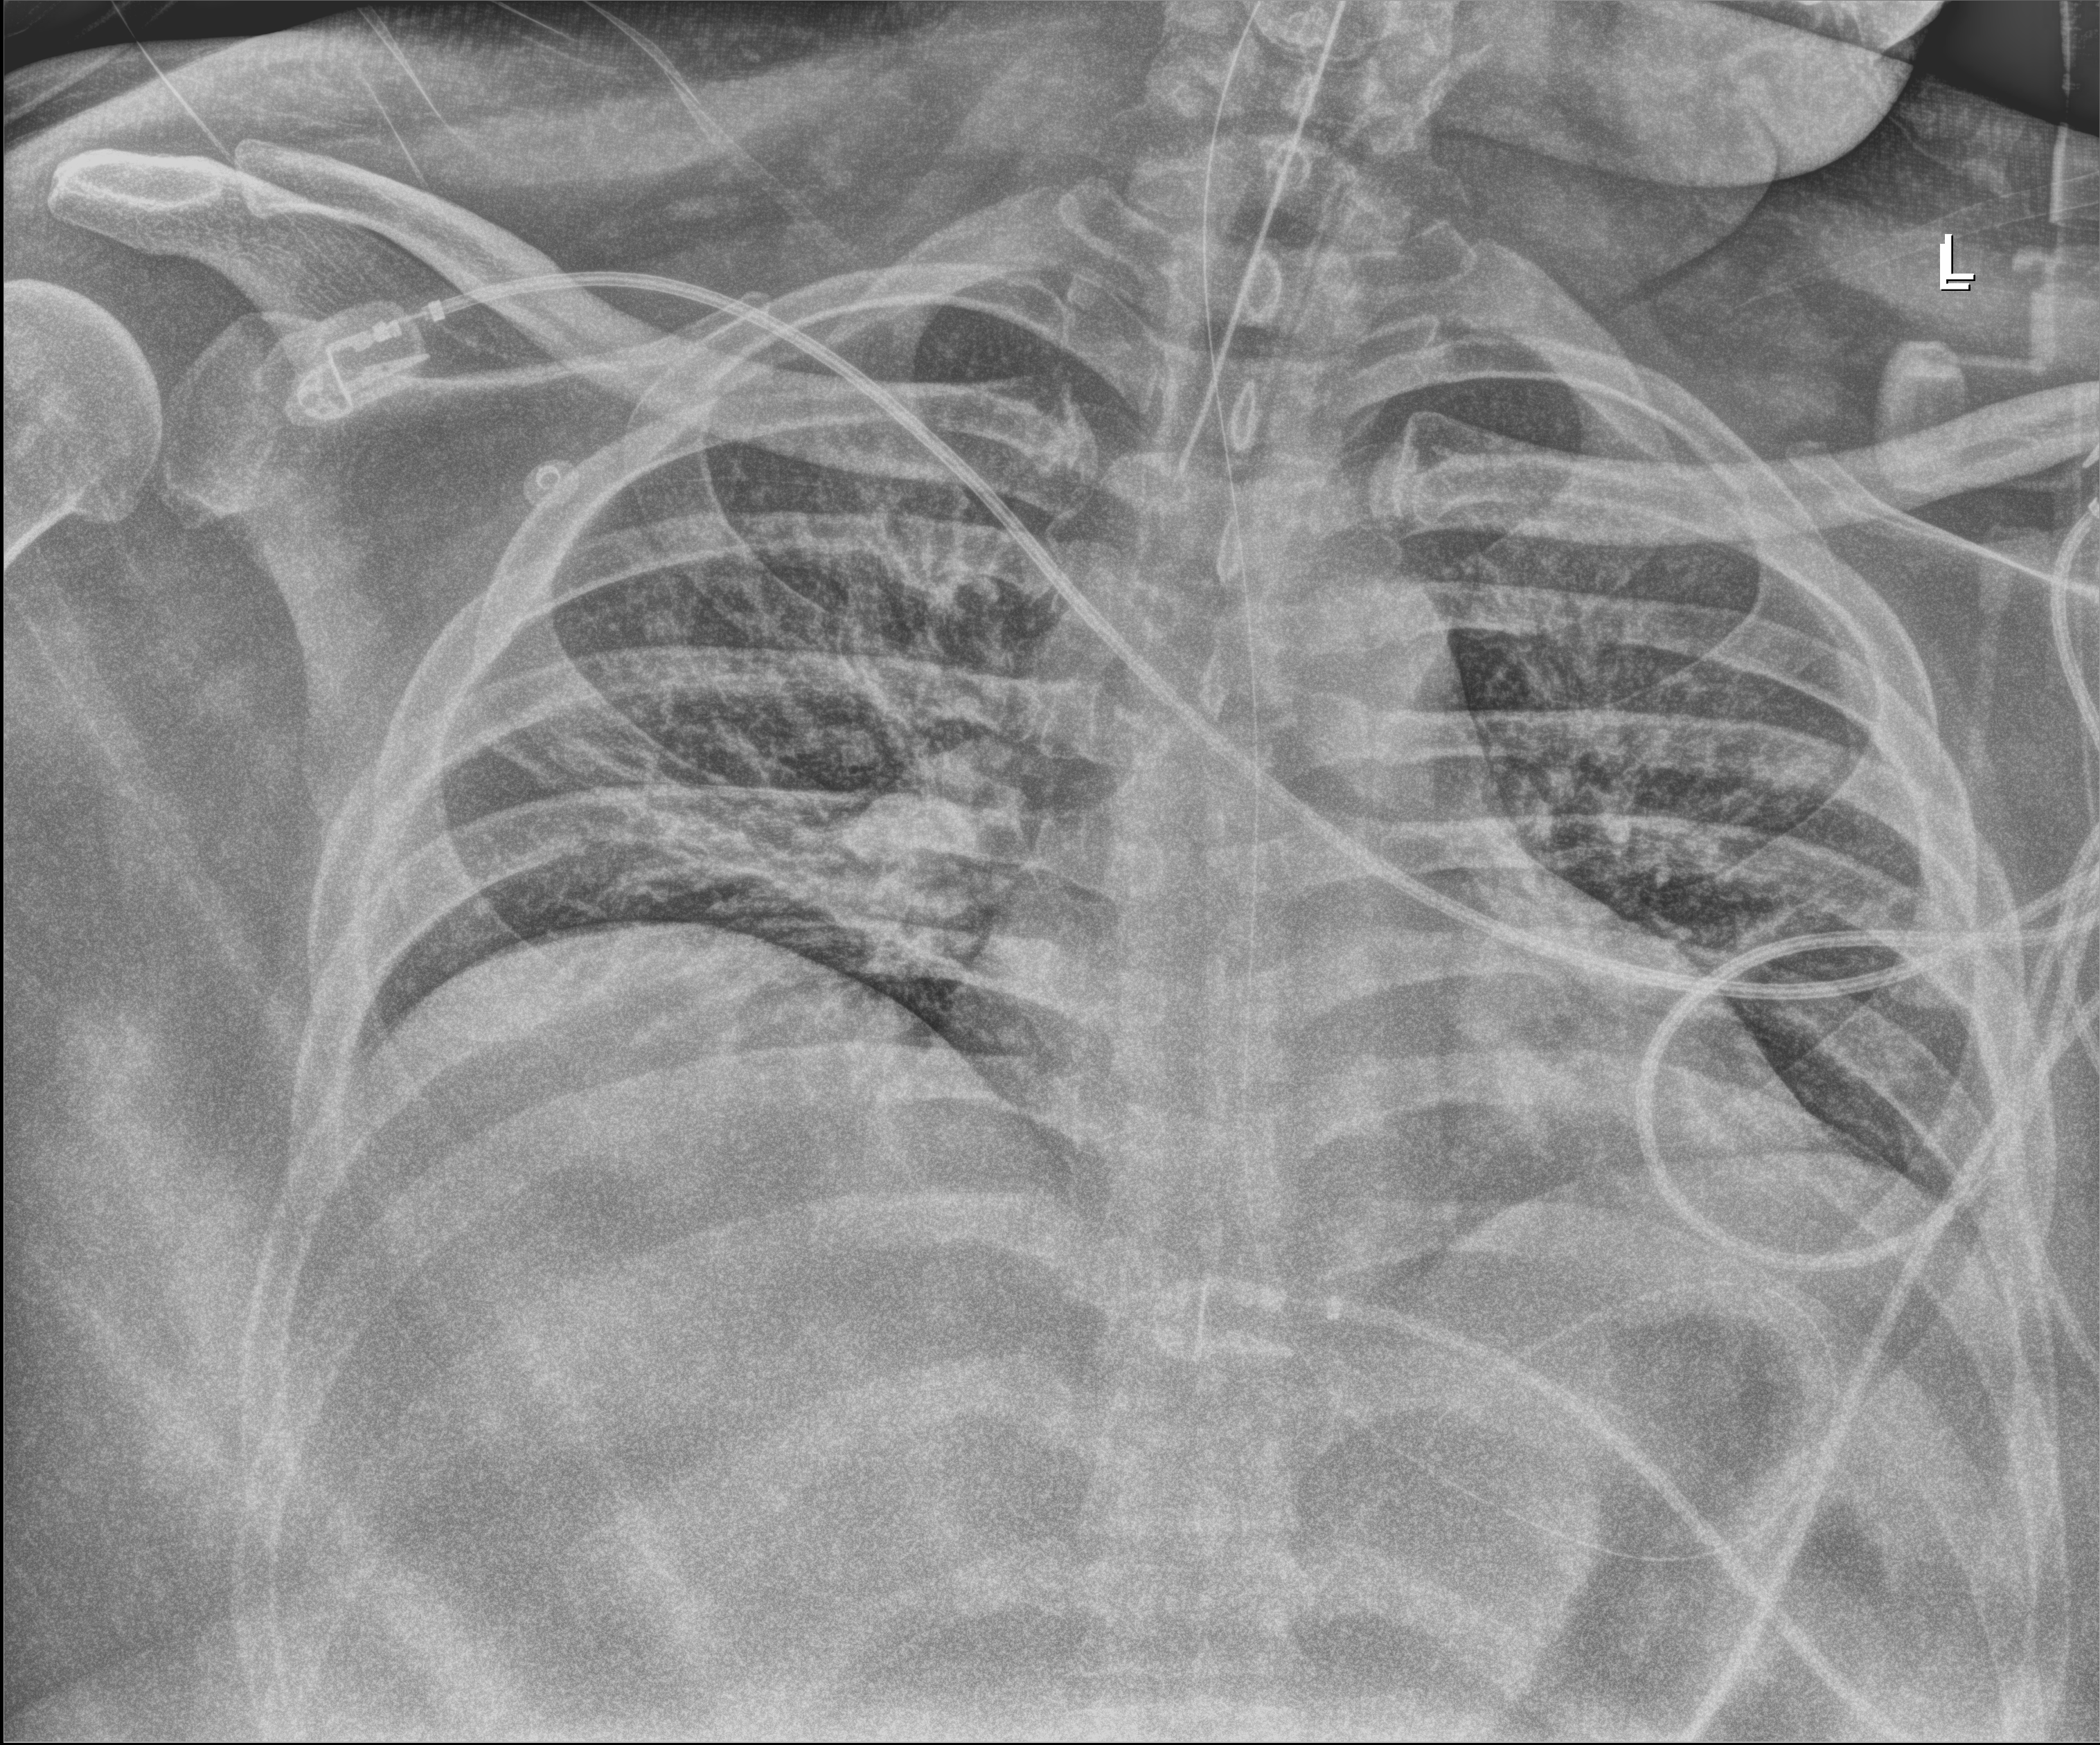
Chest X-ray (portable), anteroposterior (AP) projection. Male patient hospitalised with COVID-19, age 18–59 years.
Admission-level facts for this patient (not findings on this image; timing relative to this image not recorded):
- length of hospital stay: 69 days